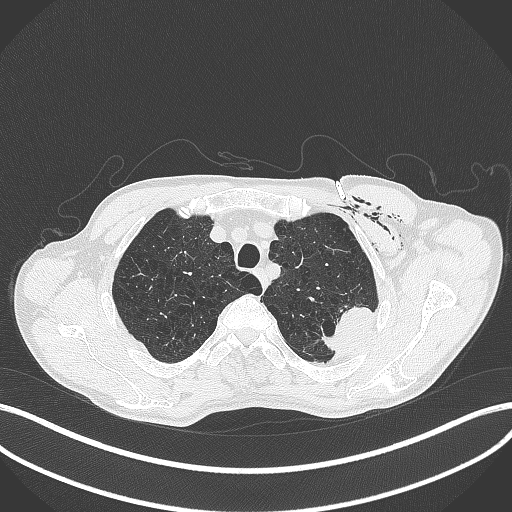
Chest CT, one axial slice; position 346 of 457 along the scan axis; reconstruction kernel B70f; lung window (W 1500 / L -600 HU); 1 mm slice thickness; 512 × 512 image matrix, field of view 400 × 400 mm. Patient: male, 58 years. Case-level facts recorded for this patient, not image findings: clinical TNM (as recorded): T3 N0 M0.
Outlined on this slice (rectangle marked by the reading radiologist):
- lung tumour (recorded histology: adenocarcinoma): box from (x=319, y=299) to (x=375, y=358) px